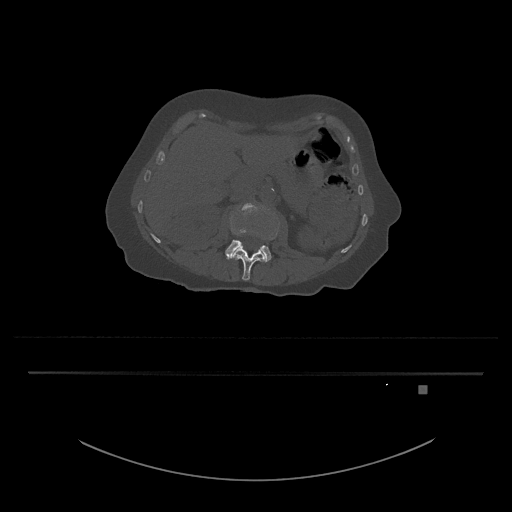
CT including the spine, one axial slice; reconstruction kernel Br40s/3; bone window (W 1800 / L 400 HU); 0.5 mm slice thickness; 512 × 512 image matrix. Female patient, age 57 years. Case-level facts recorded for this patient, not image findings: primary cancer: cervical.
Outlined on this slice (semi-automatically segmented with operator editing):
- L3 vertebra: box from (x=225, y=202) to (x=279, y=262) px